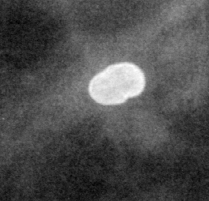
Region of interest cut from a scanned film mammogram (one marked finding); left breast; CC view; BI-RADS breast density category 2 (scale 1–4).
Calcifications, morphology lucent center; BI-RADS assessment category 2; benign without callback (not worked up further).